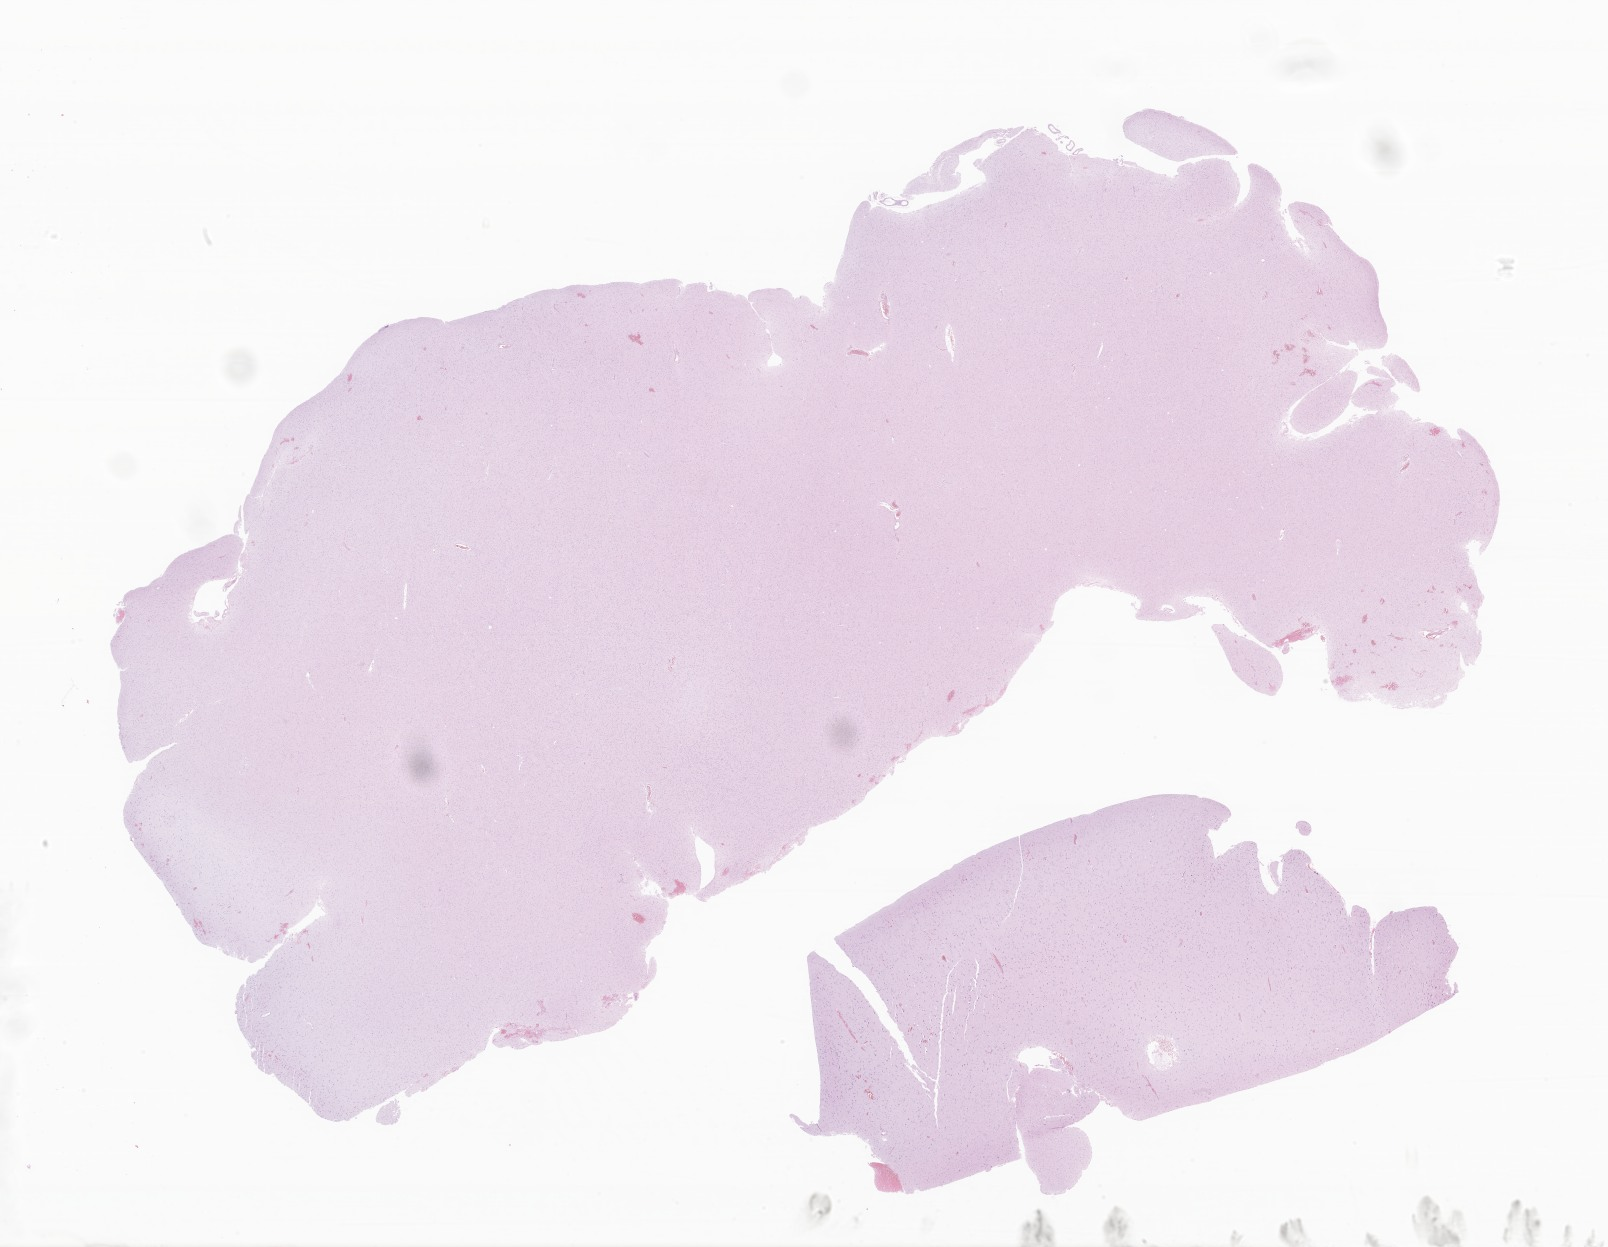
Hematoxylin and eosin (H&E) whole-slide image of tumor tissue from the brain — shown as a low-resolution overview of the whole scanned area (about 27.1 x 21.0 mm); formalin-fixed paraffin-embedded section. Patient: male, age 274 months (22 years 10 months).
* diagnosis (ICD-O-3 morphology term): Astrocytoma, NOS